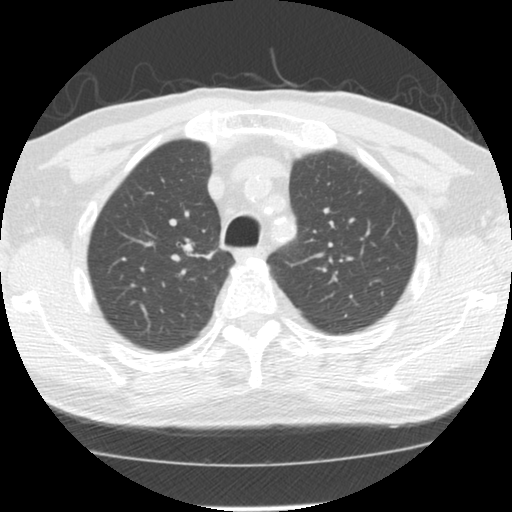
Chest CT (low-dose screening protocol), one axial image. Baseline annual screen. Lung window (W 1500 / L -600 HU). 2.5 mm slice thickness. Slice 36 of 139 in the series. 512 × 512 image matrix, field of view 310 × 310 mm. Male, age 64 years at enrolment. Former smoker at enrolment.
- Expert reader's lesion annotation, bounding box <170,232,224,276> (left, top, right, bottom; pixels).
- Reader record for this screening exam (exam-level; its link to the box is not recorded): non-calcified nodule or mass ≥4 mm, right upper lobe, 20 × 13 mm, spiculated (stellate) margins, soft tissue attenuation.
- Official screen result: positive, change unspecified: nodule(s) >= 4 mm or enlarging nodule(s), mass(es), or other non-specific abnormalities suspicious for lung cancer.
- Participant outcome: lung cancer diagnosed 73 days after this screen — adenocarcinoma, NOS, right upper lobe, moderately differentiated (G2), stage IA (AJCC 6th edition), 17 mm at pathology.